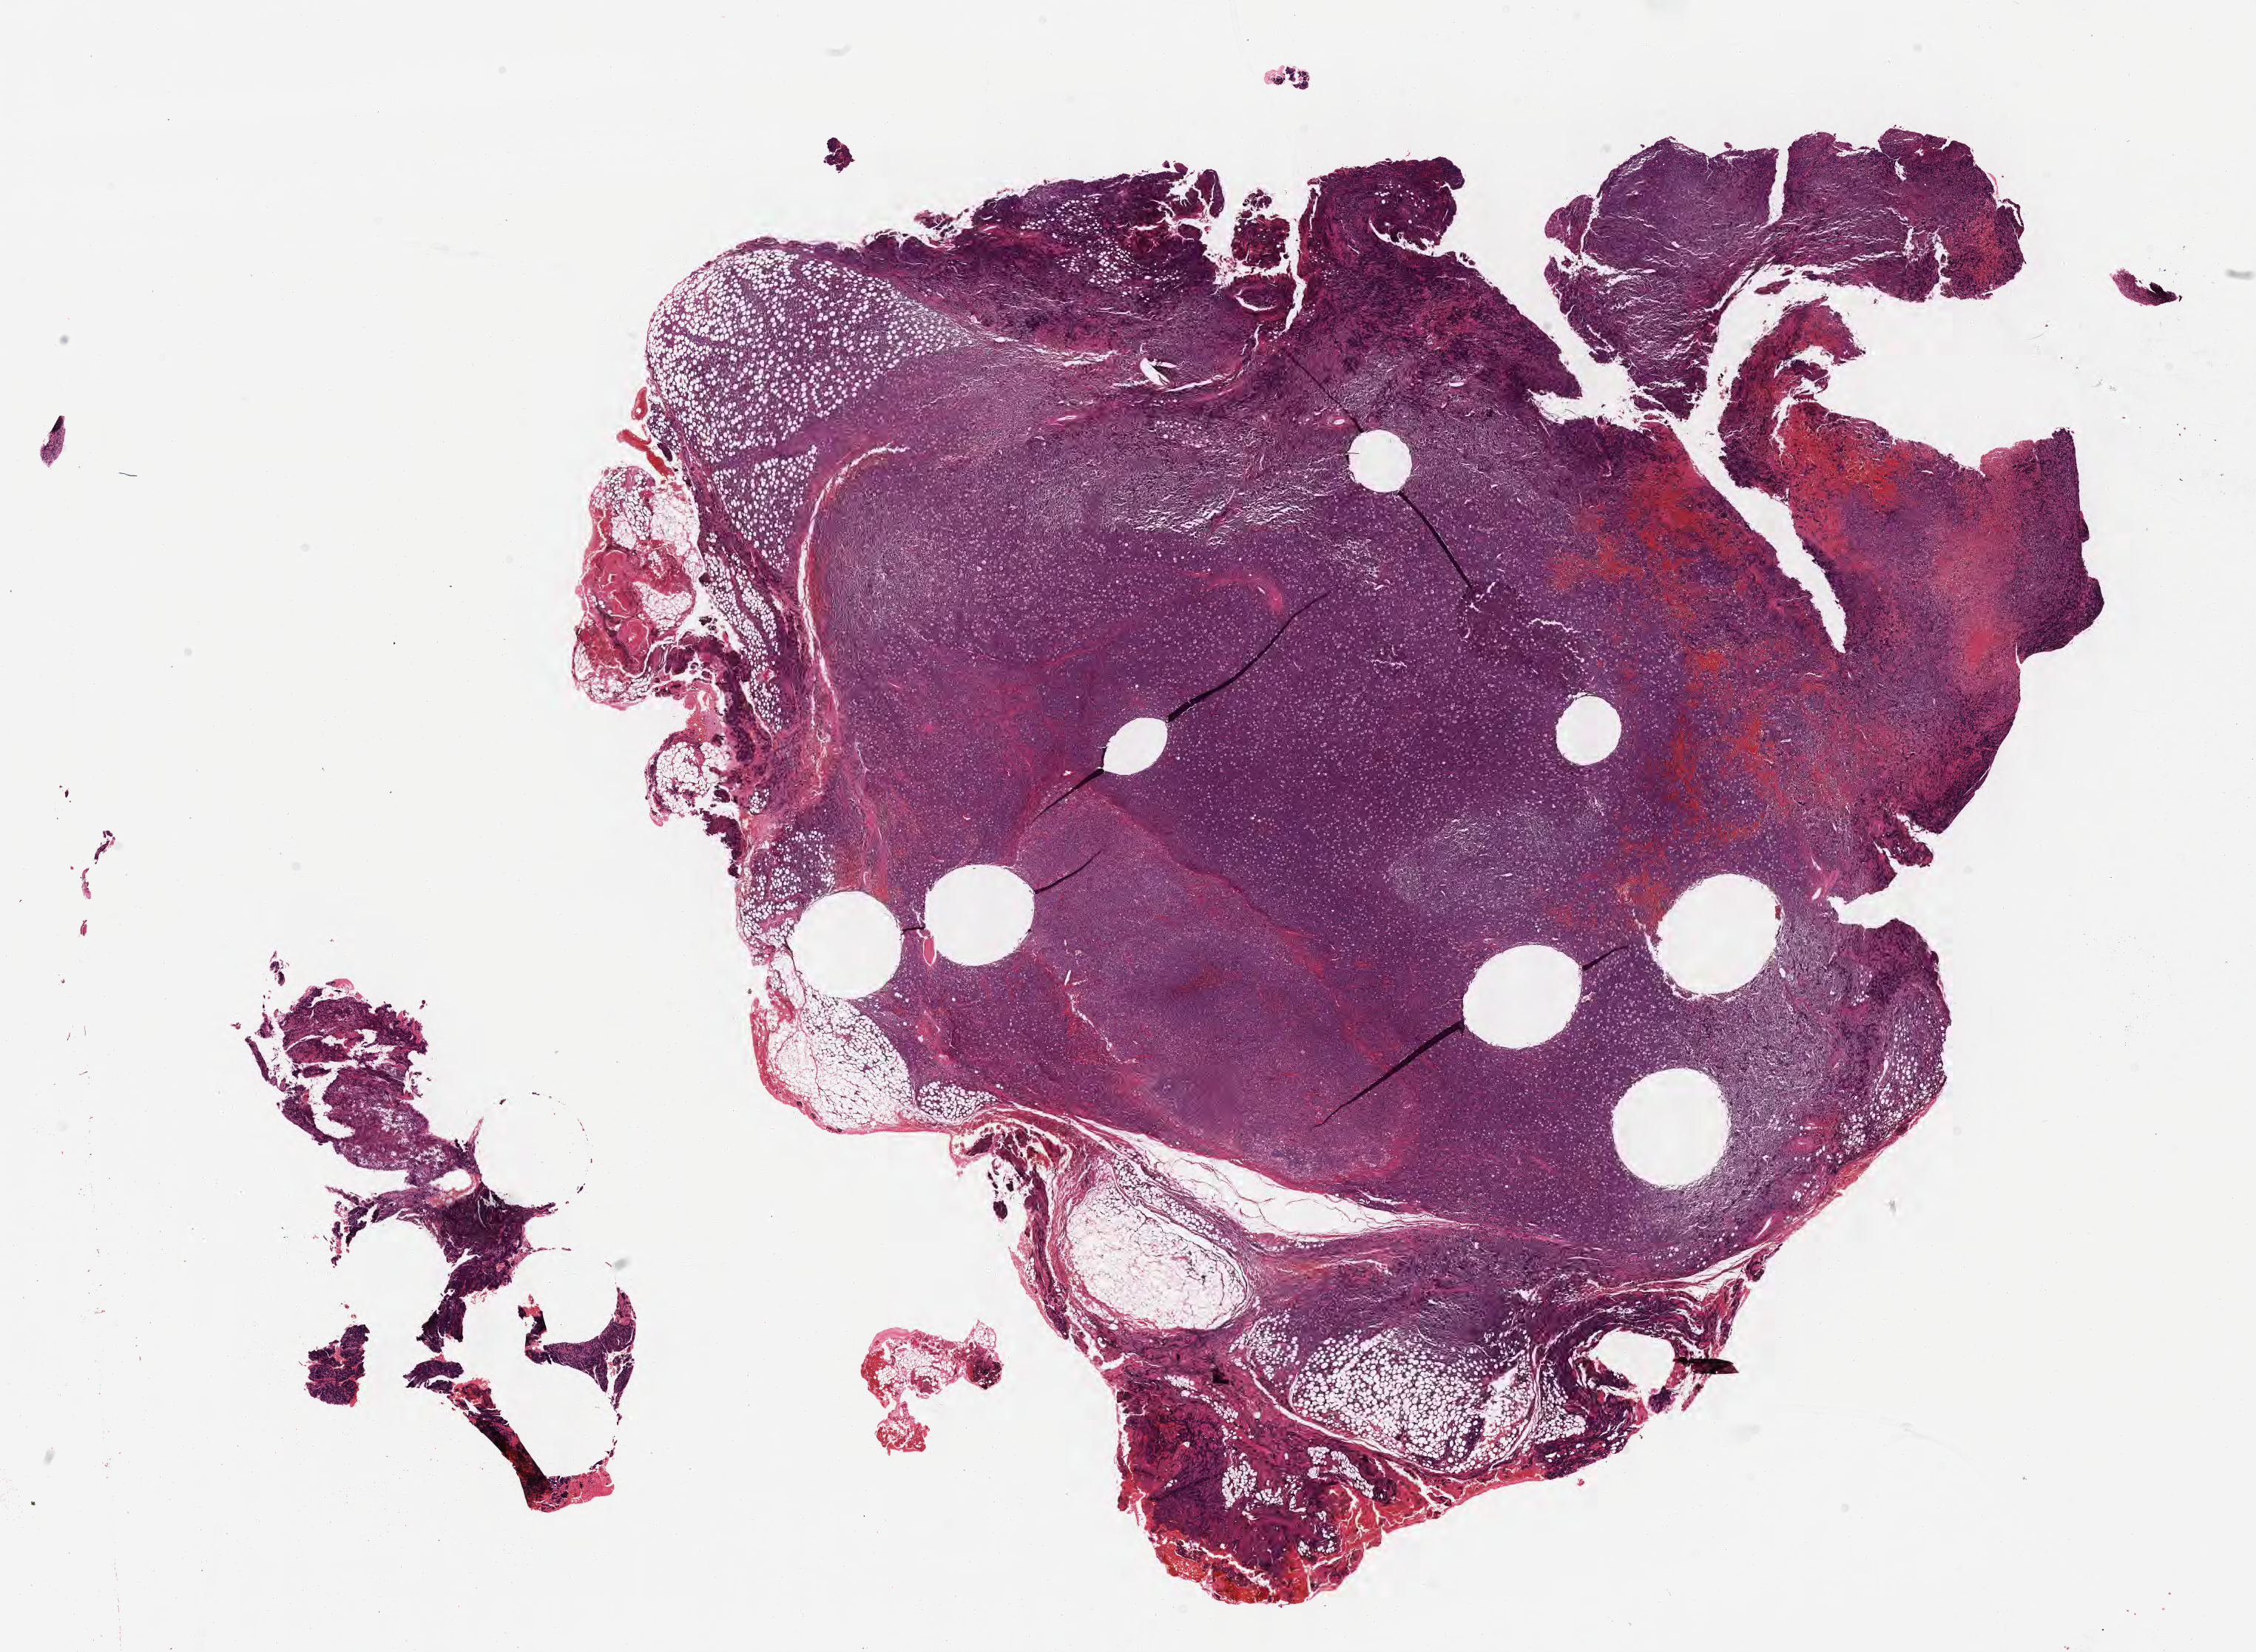
Haematoxylin and eosin whole-slide image, whole scanned area (about 24.6 x 18.1 mm) shown as a low-resolution overview; formalin-fixed paraffin-embedded section; primary tumor. Patient male; 40 years old. Composition of this section per pathologist review: tumor cells 80%, tumor nuclei 90%, stromal cells 10%, necrosis 5%, normal cells 5%. Inflammatory infiltration, as recorded: lymphocyte infiltration 25%, monocyte infiltration 40%, neutrophil infiltration 5%.
Section: bottom of the tissue portion.